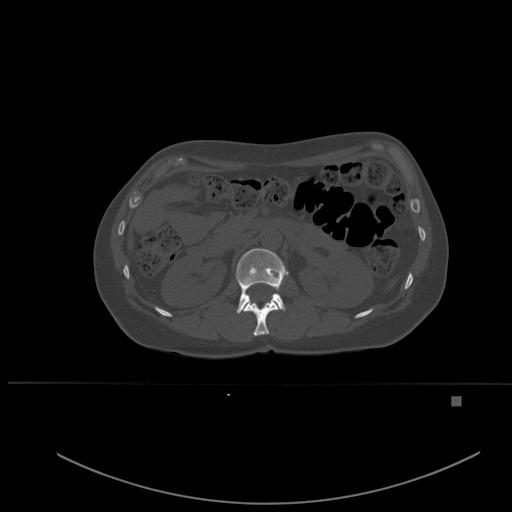
CT including the spine, one axial slice; position 242 of 651 along the scan axis; bone window (W 1800 / L 400 HU); 1.5 mm slice thickness; 512 × 512 image matrix, field of view 443 × 443 mm. Patient: female, 49 years. From the clinical record (not read from this slice): primary cancer: breast; vertebrae with lytic lesions (as recorded): L3, T12, L4.
Annotated regions visible in this slice (semi-automatically segmented with operator editing):
- L1 vertebra: bounding box <236,248,289,314> (left, top, right, bottom; pixels)
- T12 vertebra: <243,300,279,336>